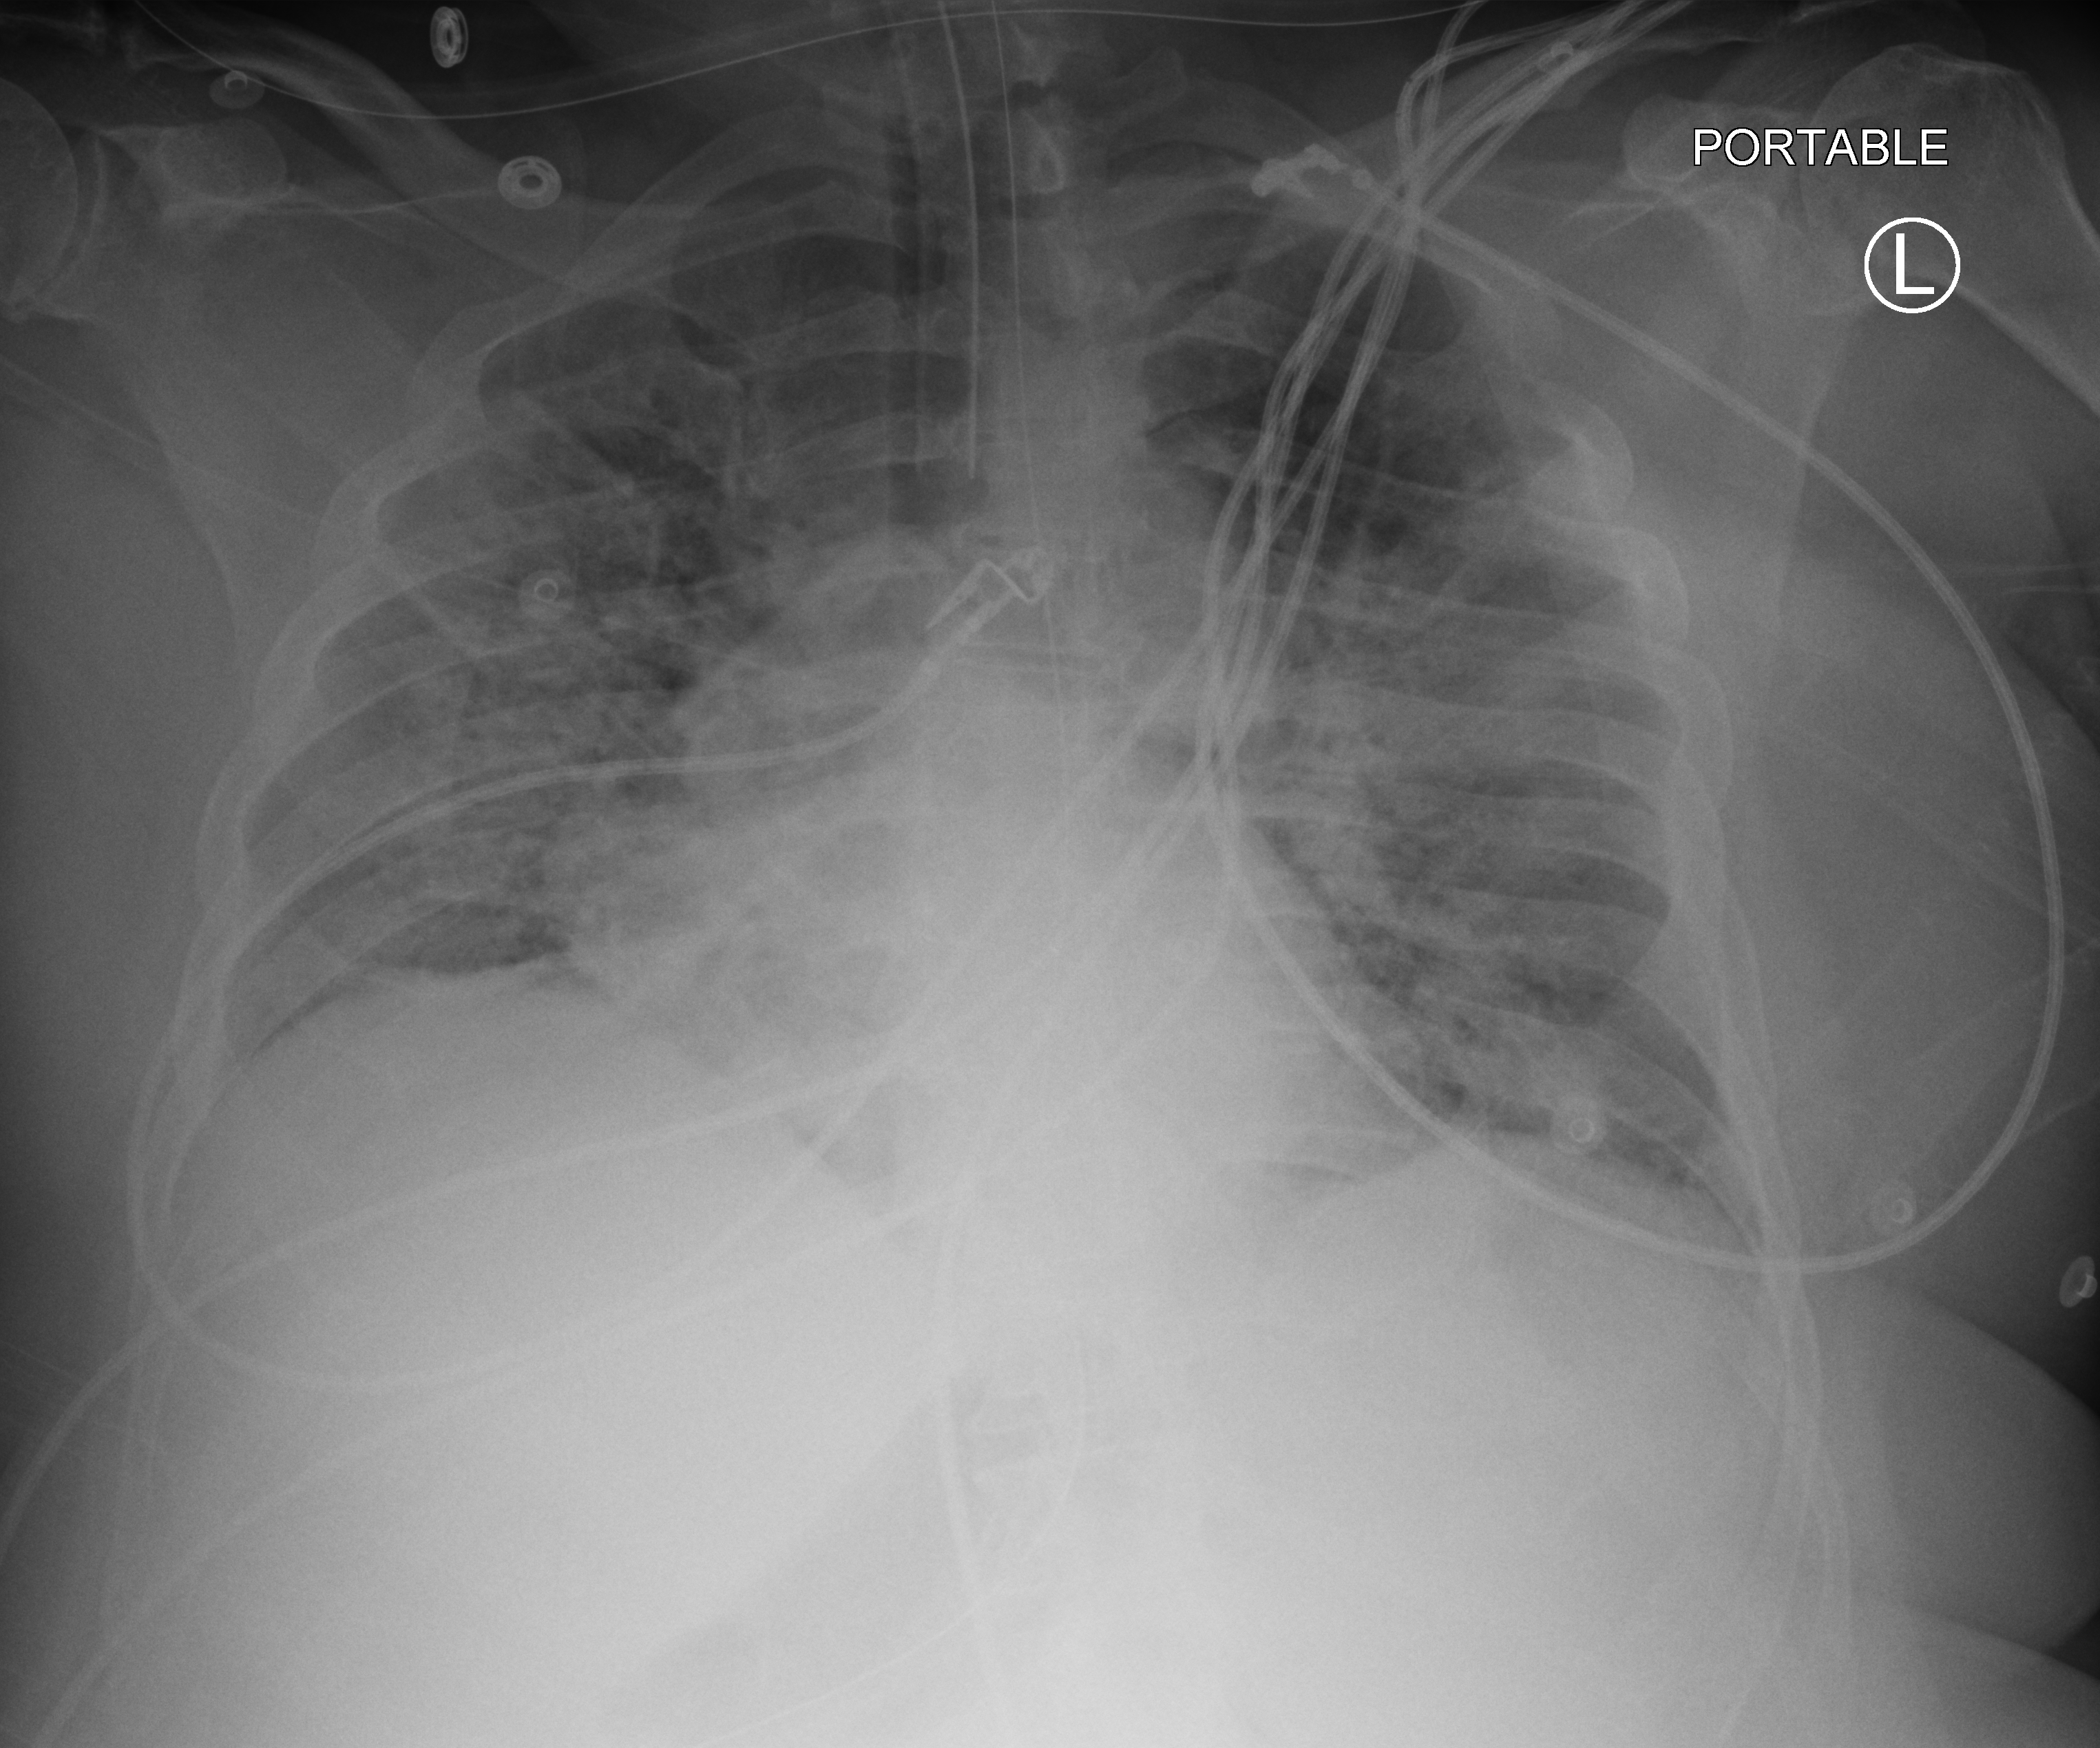
Portable chest radiograph, anteroposterior (AP) projection. Male patient hospitalised with COVID-19, age 18–59 years.
Admission-level facts for this patient (not findings on this image; timing relative to this image not recorded): mechanically ventilated during this hospital stay: yes; admitted to intensive care during this hospital stay: yes; other chronic lung disease (admission record): yes.